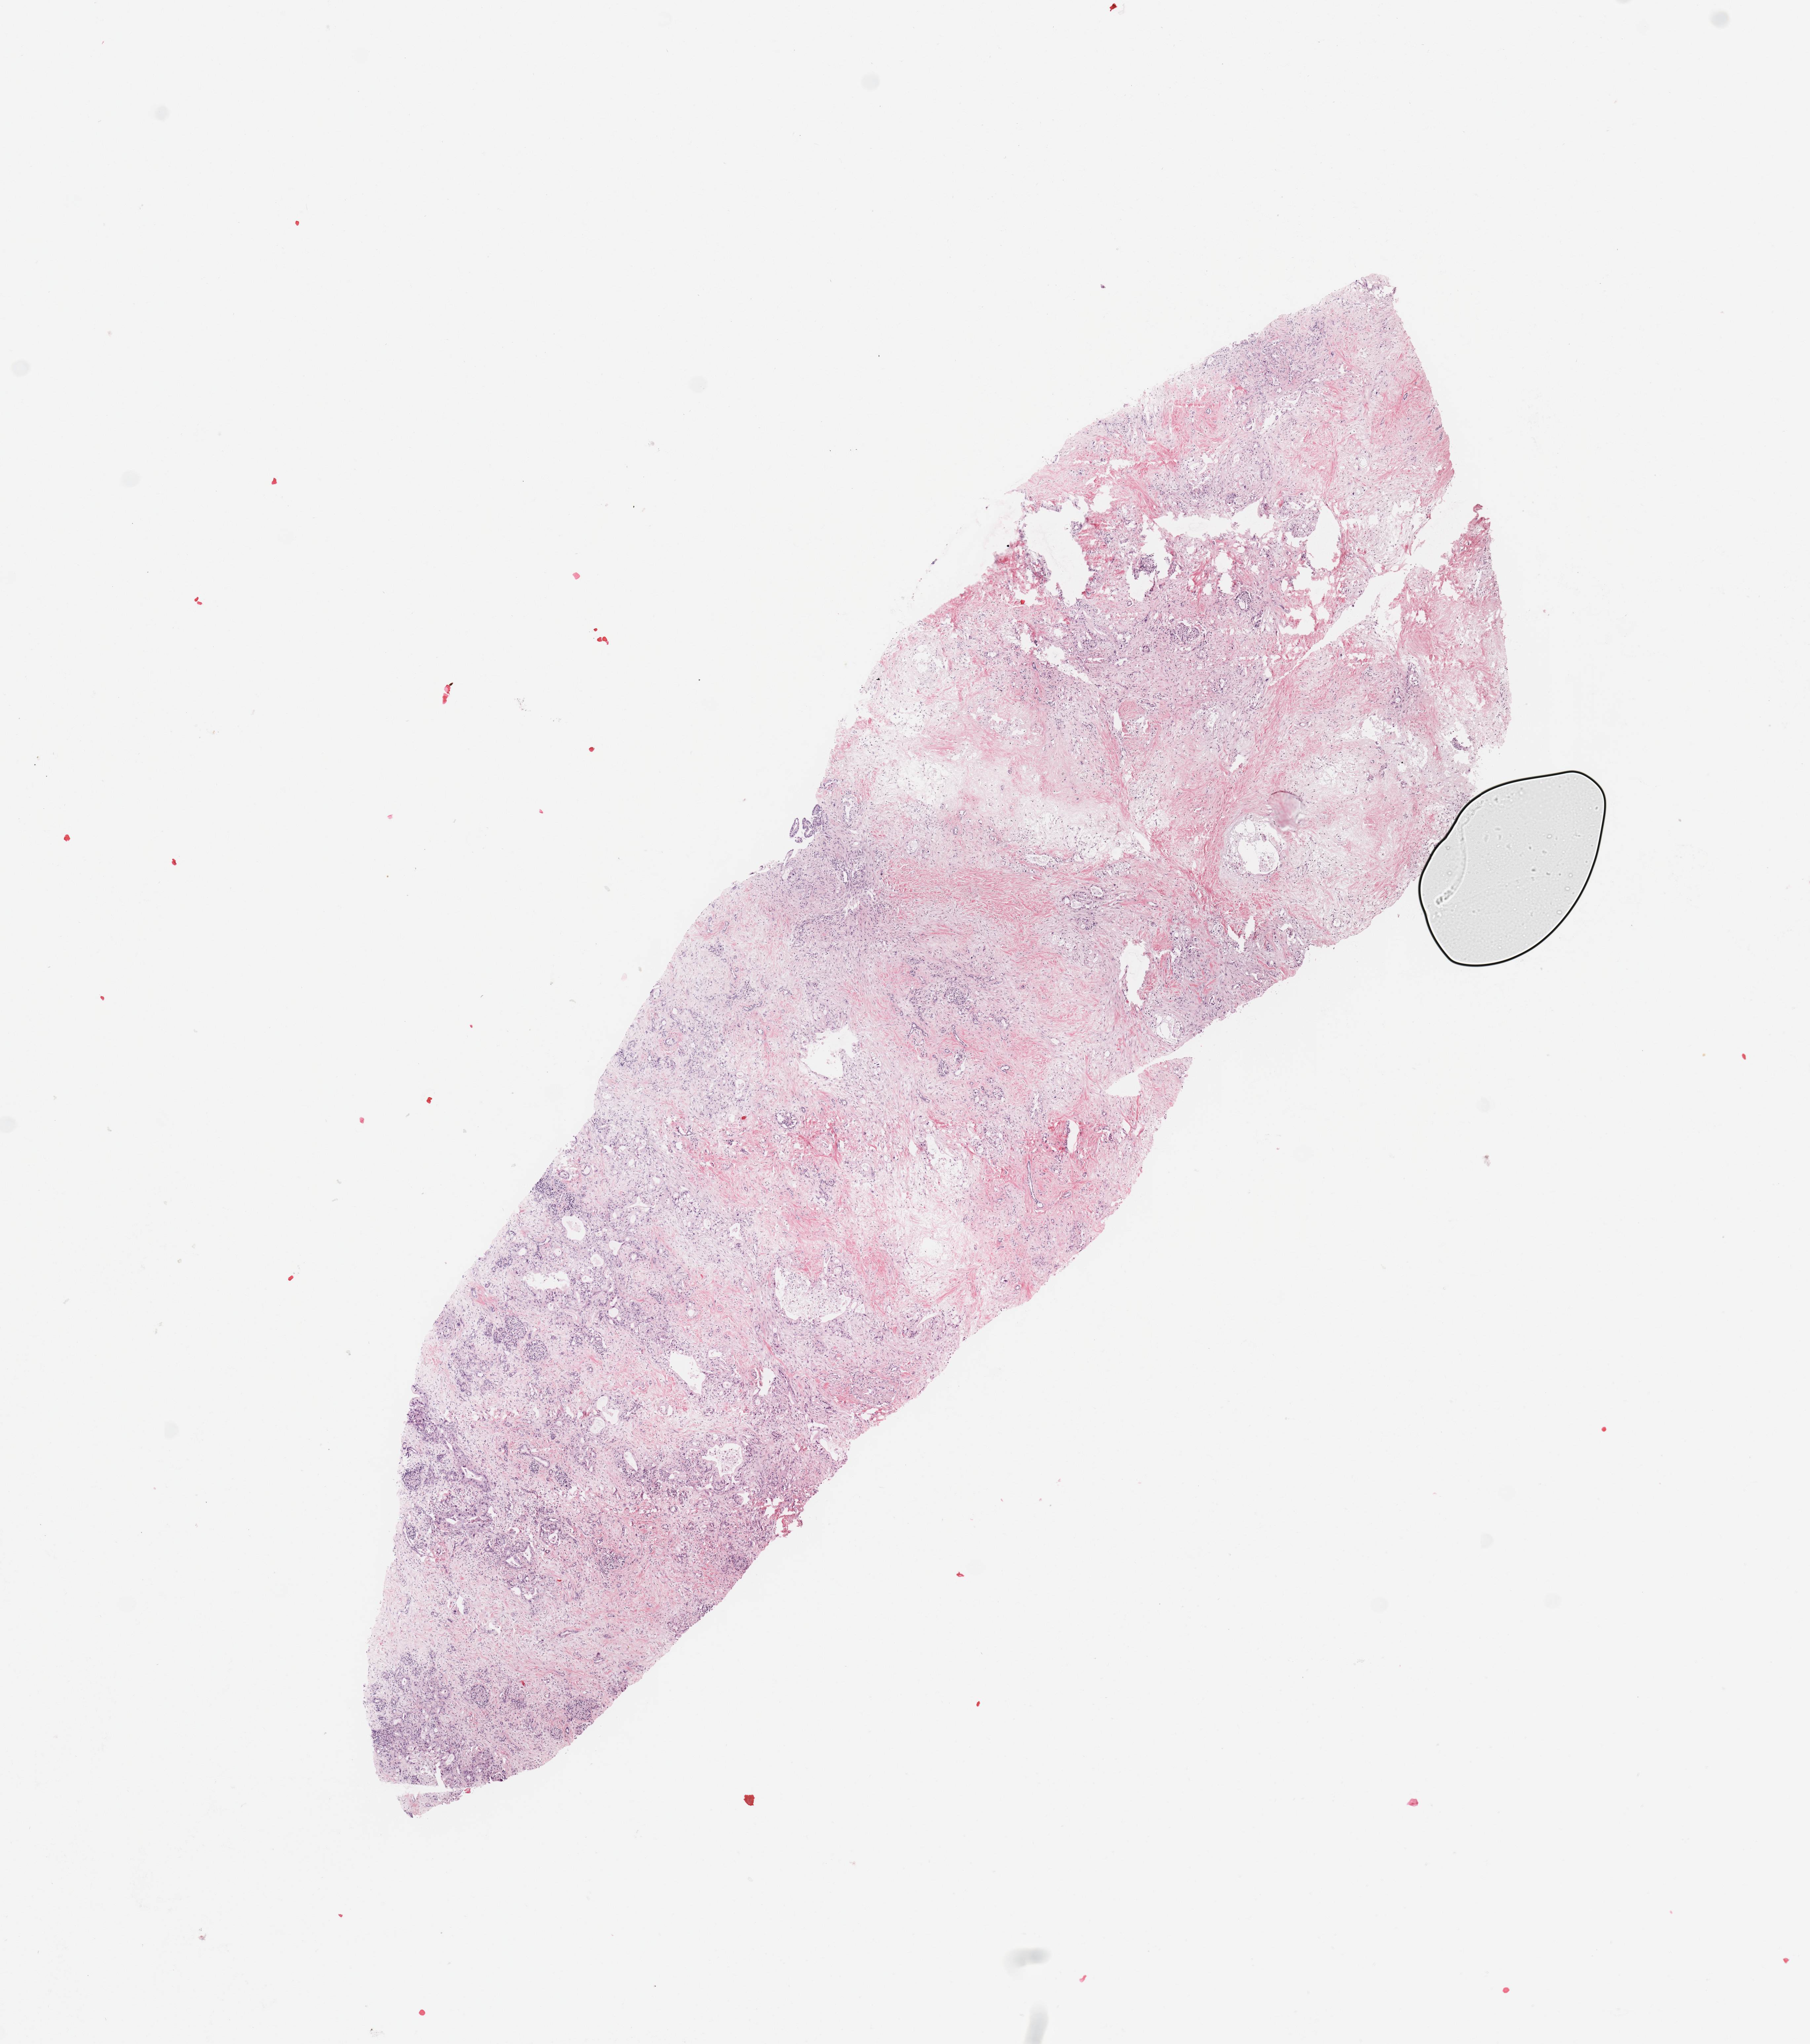
H&E-stained whole-slide image, a low-resolution overview of the entire scanned area, about 10.8 x 12.2 mm (from a 20x scan); tumour tissue sample, sampled site: pancreas. Male, 54 y/o. Histologic grade: G2 (moderately differentiated). Composition of this section per pathologist review: tumour nuclei 40%, necrosis 5%.
* AJCC pathologic stage: IIB
* diagnosis: Infiltrating duct carcinoma, NOS
* primary tumour site (as recorded): tail